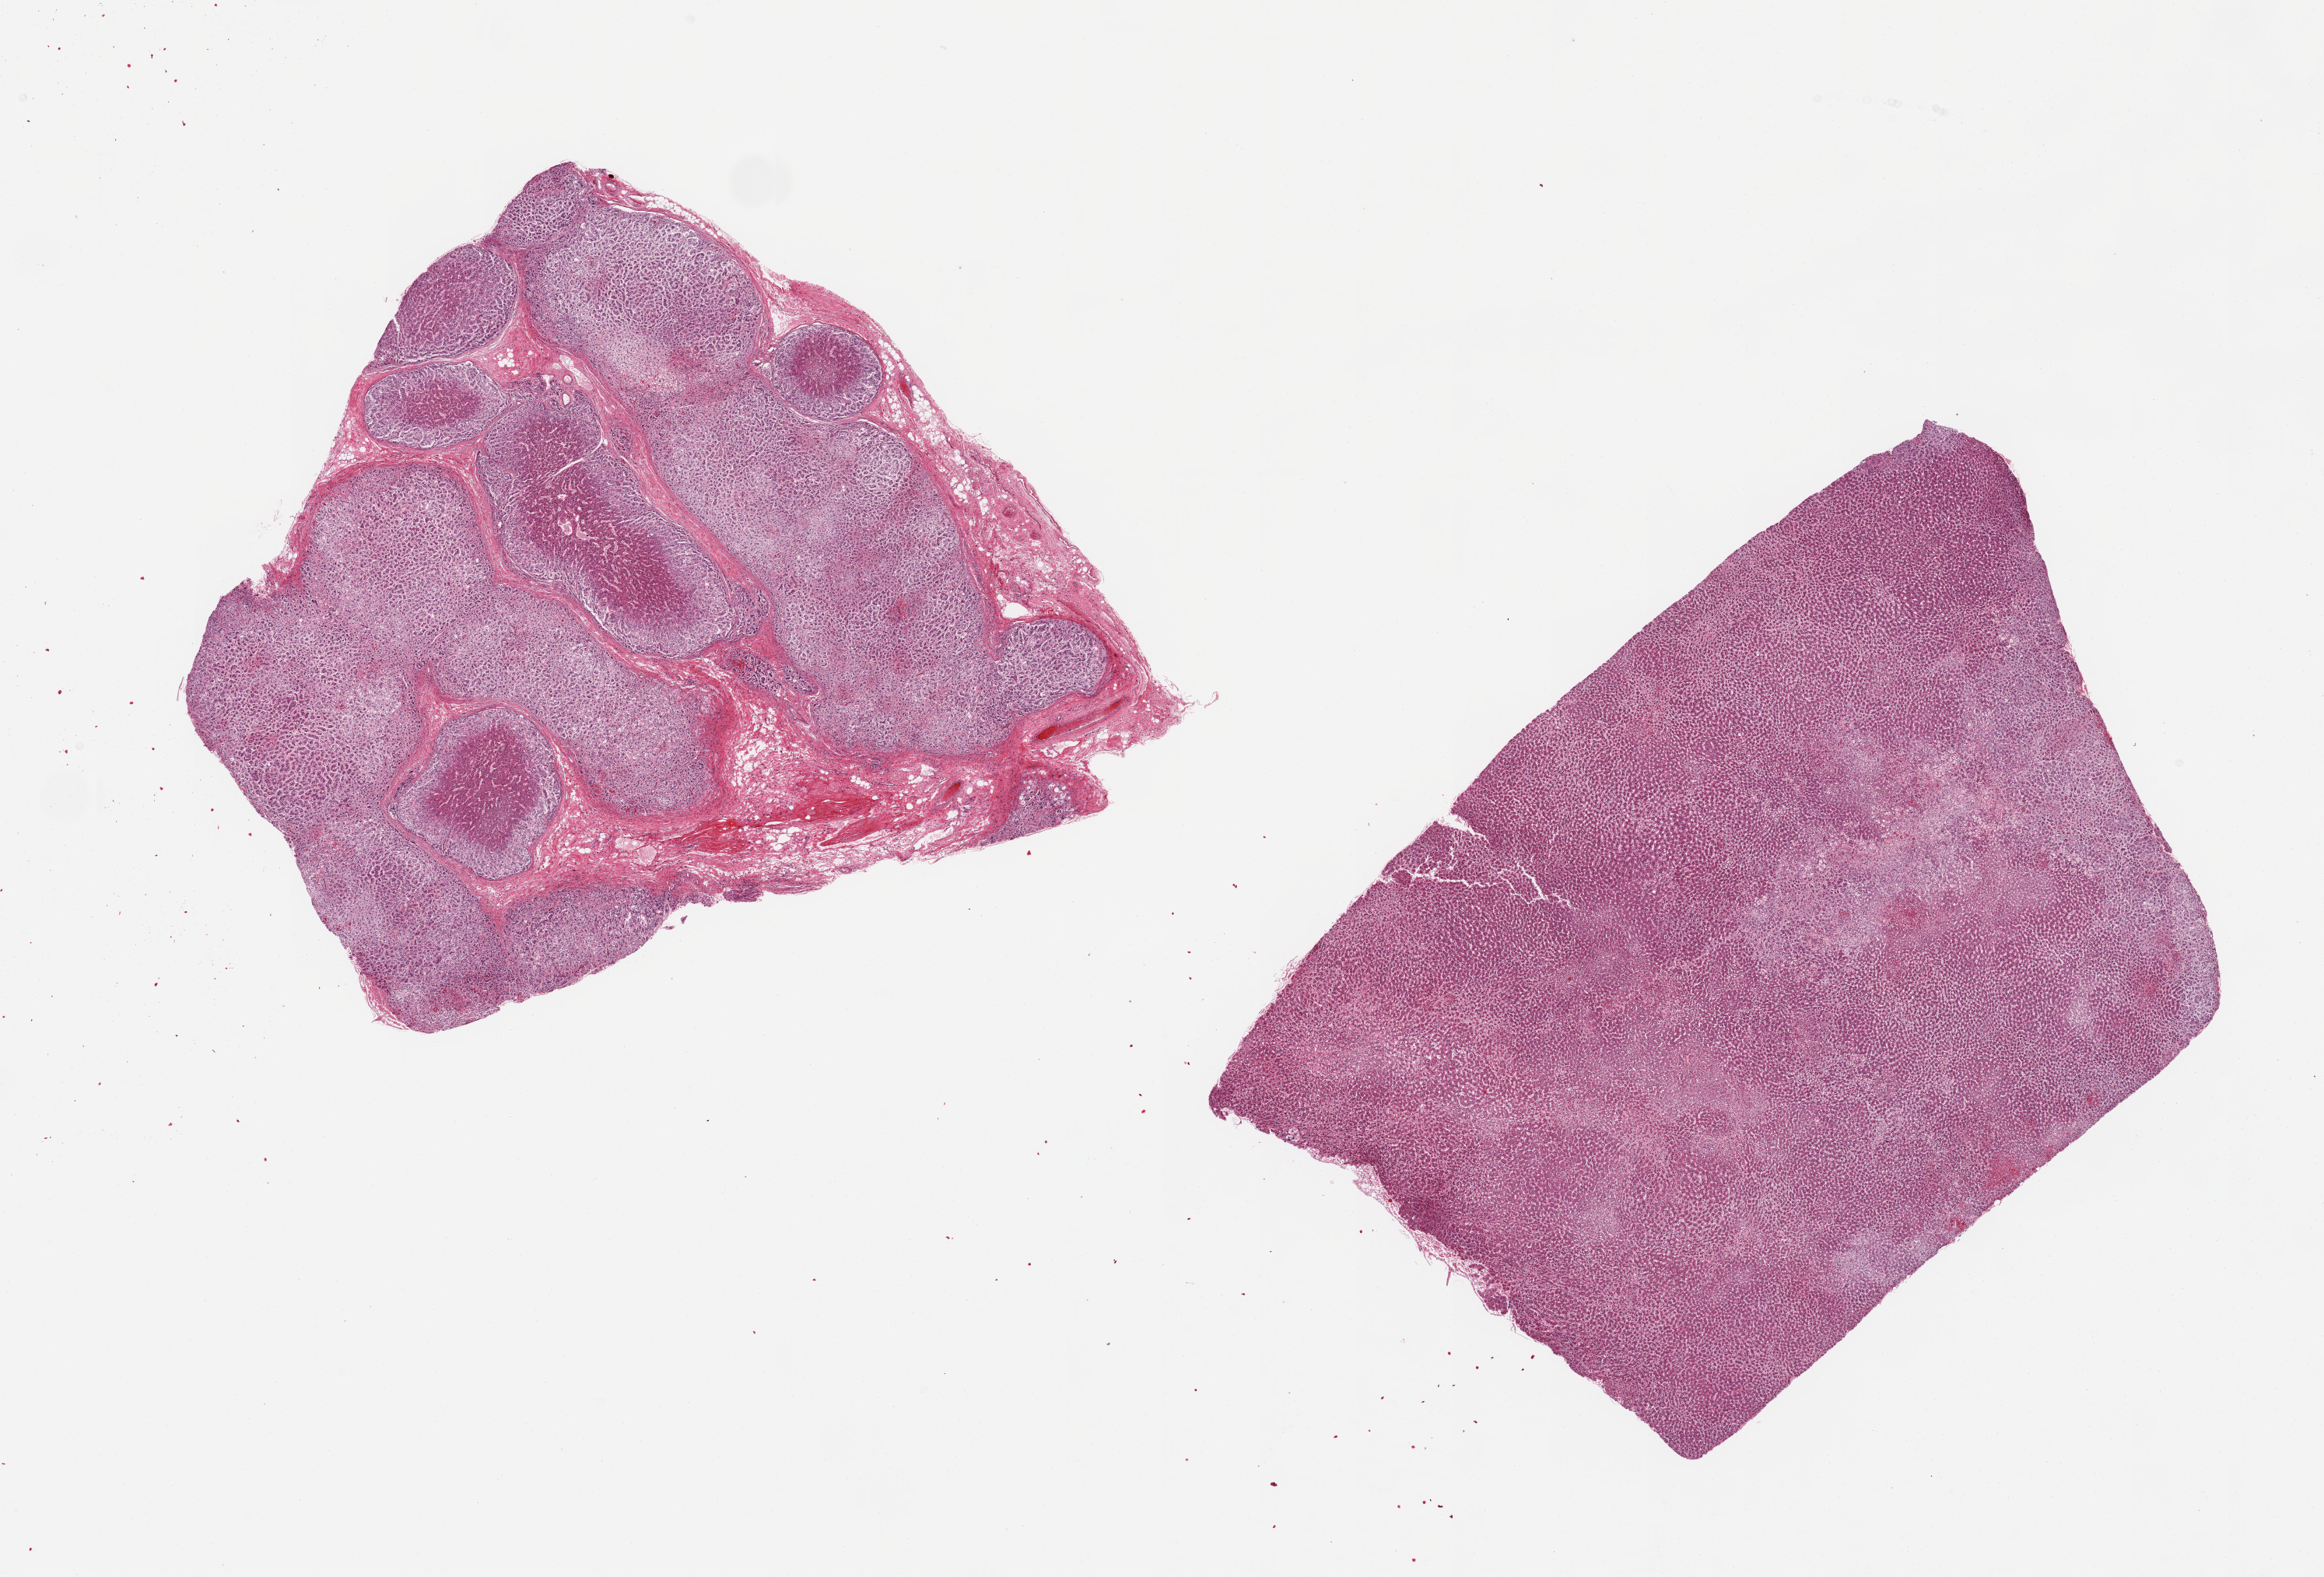
Haematoxylin and eosin whole-slide image — shown as a low-resolution overview of the whole scanned area (about 23.6 x 16.0 mm); PAXgene-fixed paraffin-embedded (PFPE) section; target tissue: adrenal gland; donor tissue sample. Donor sex: male.
* review note (as recorded): 2 pieces, cortex; moderately advanced autolysis